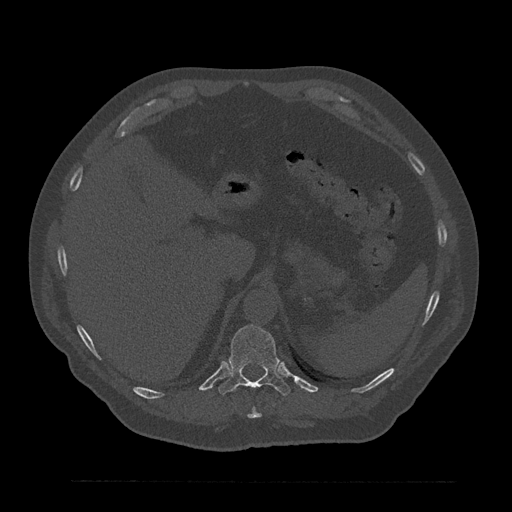
CT including the spine, one axial slice. Position 303 of 797 along the scan axis. Reconstruction kernel Br40s/3. 120 kVp. Bone window (W 1800 / L 400 HU). 0.5 mm slice thickness. 512 × 512 image matrix. Male patient, age 61 years. Case-level facts recorded for this patient, not image findings: primary cancer: prostate.
Structures marked on this image (semi-automatic segmentation, software-assisted and operator-edited):
- T10 vertebra: bounding box [x1, y1, x2, y2] px = [247, 407, 262, 419]
- T11 vertebra: [219, 325, 290, 396]